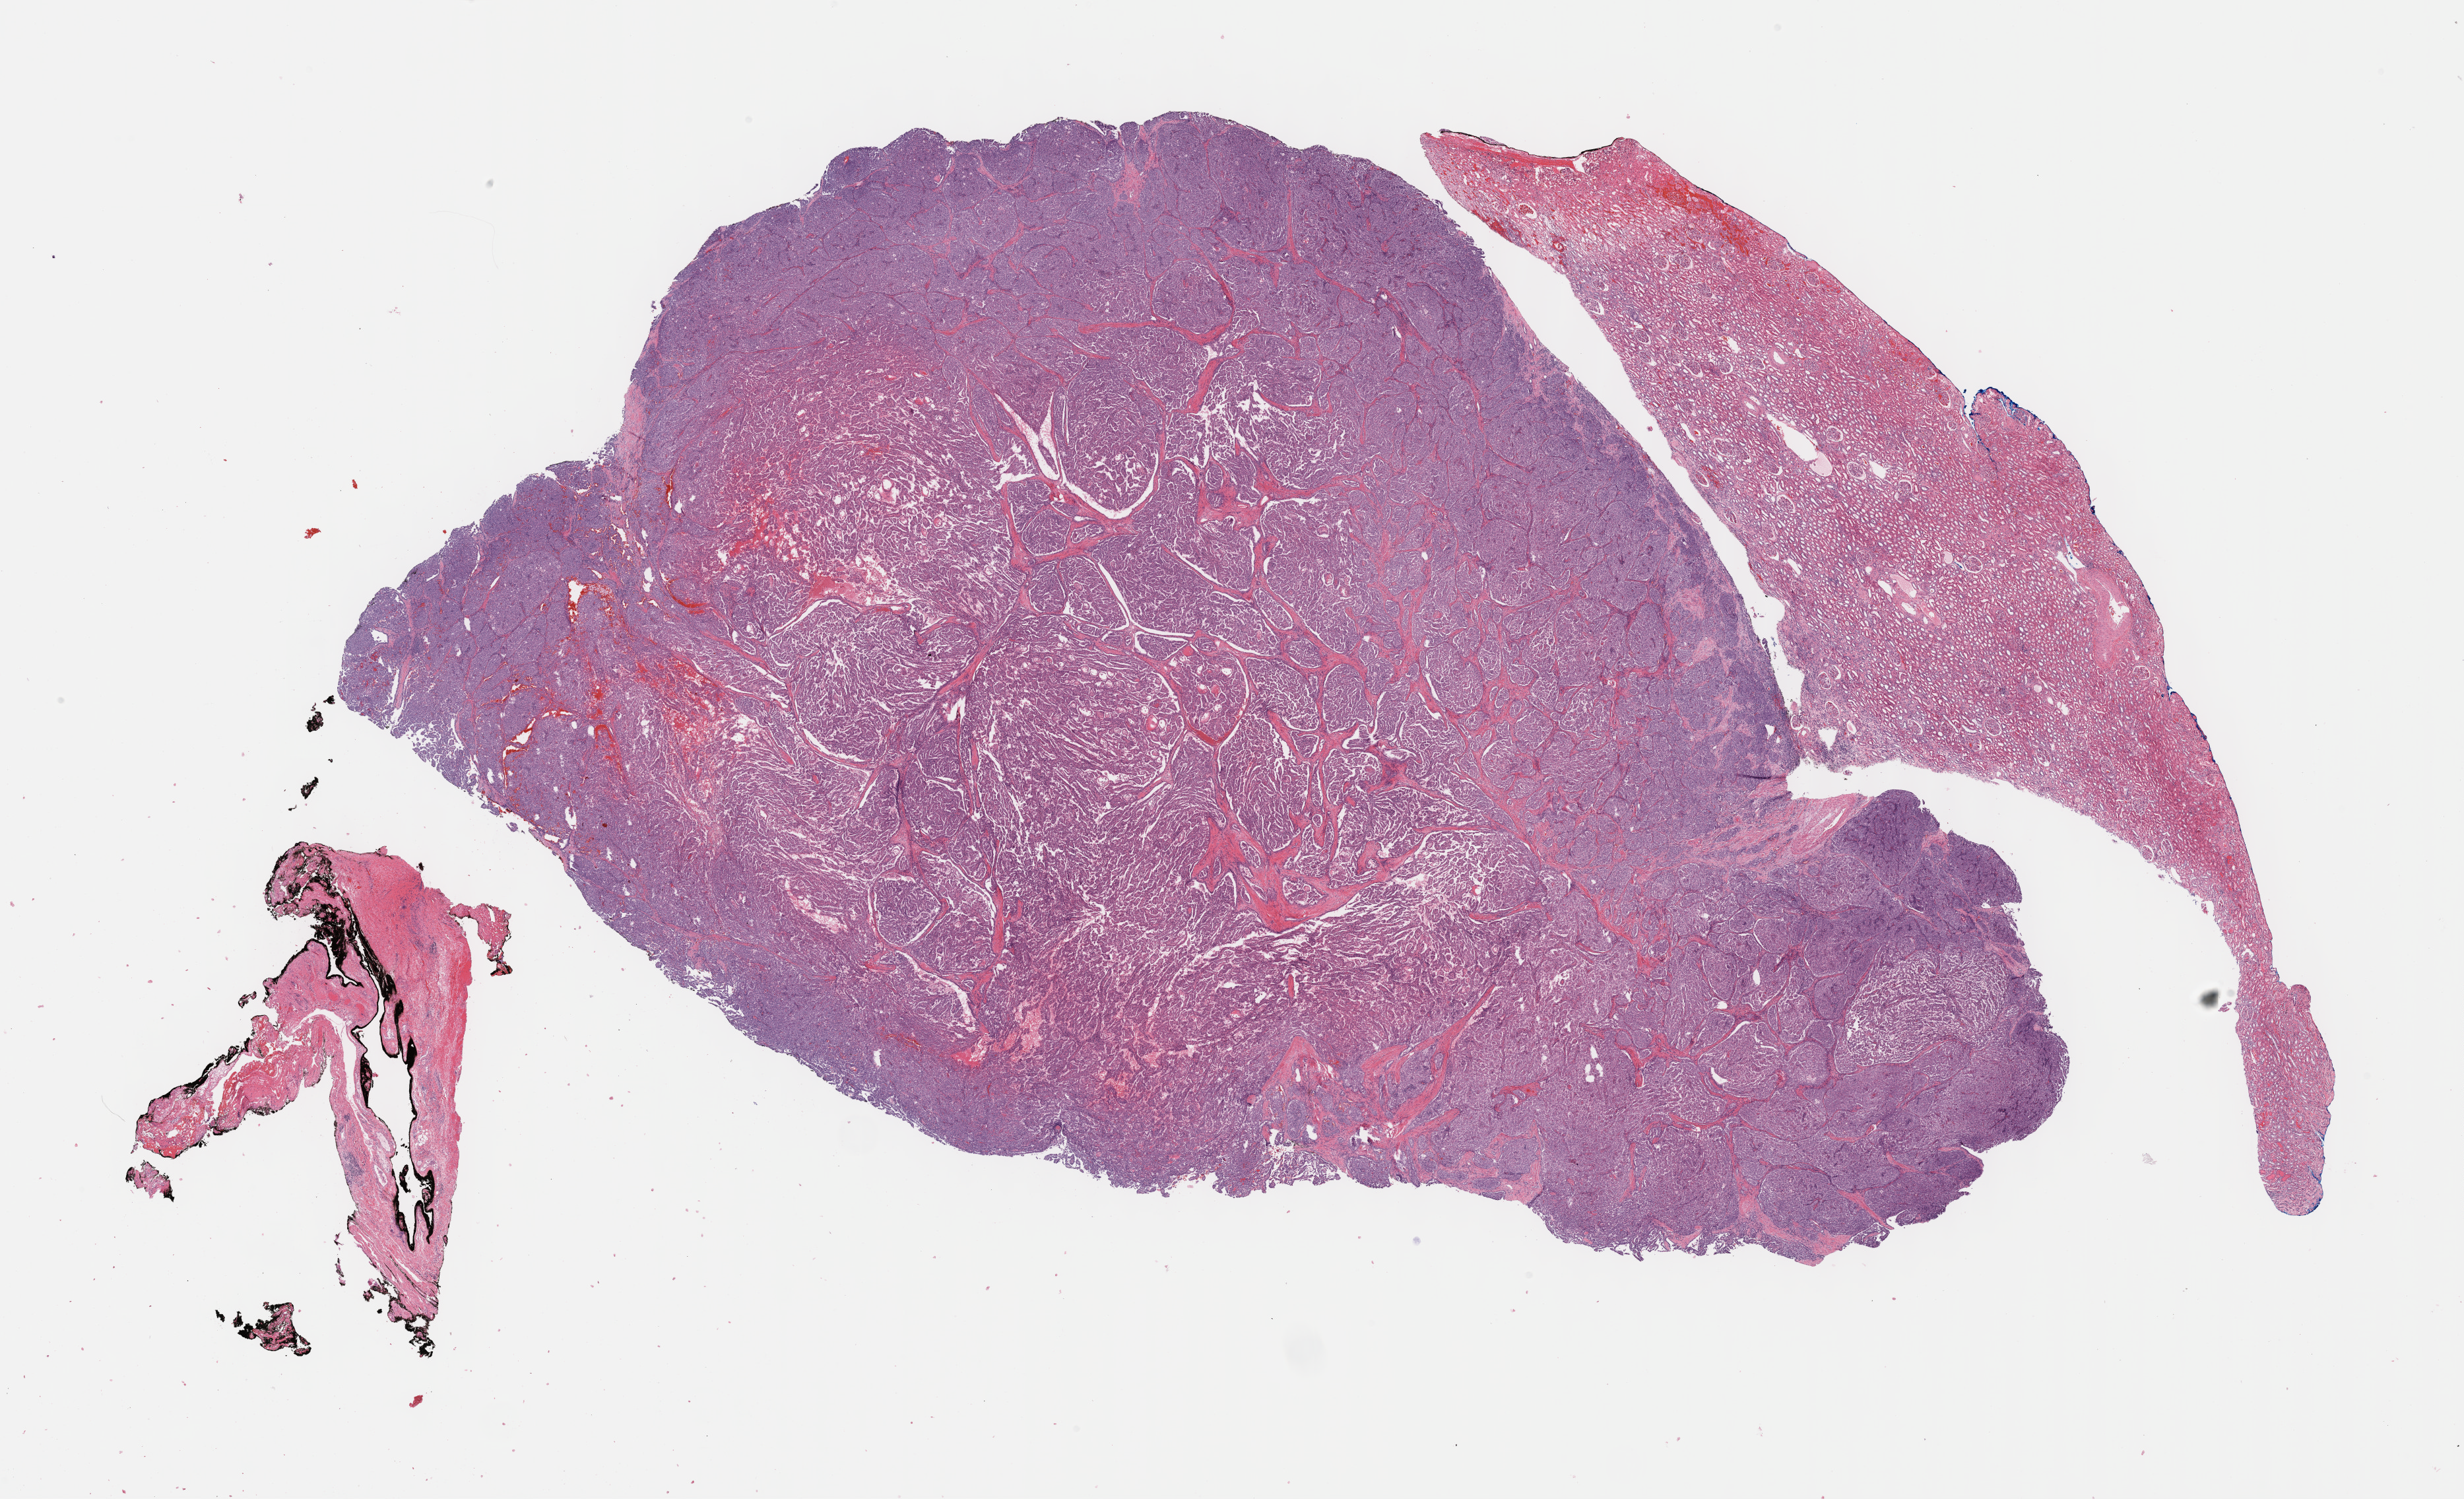
H&E-stained whole-slide image — shown as a low-resolution overview of the whole scanned area (about 30.2 x 18.4 mm). Formalin-fixed paraffin-embedded (FFPE) diagnostic section. Kidney, primary tumour sample. Male, age 54 years at initial diagnosis.
- laterality: right
- diagnosis: Papillary adenocarcinoma, NOS
- TNM: T1a NX M0
- AJCC pathologic stage: I (7th edition)